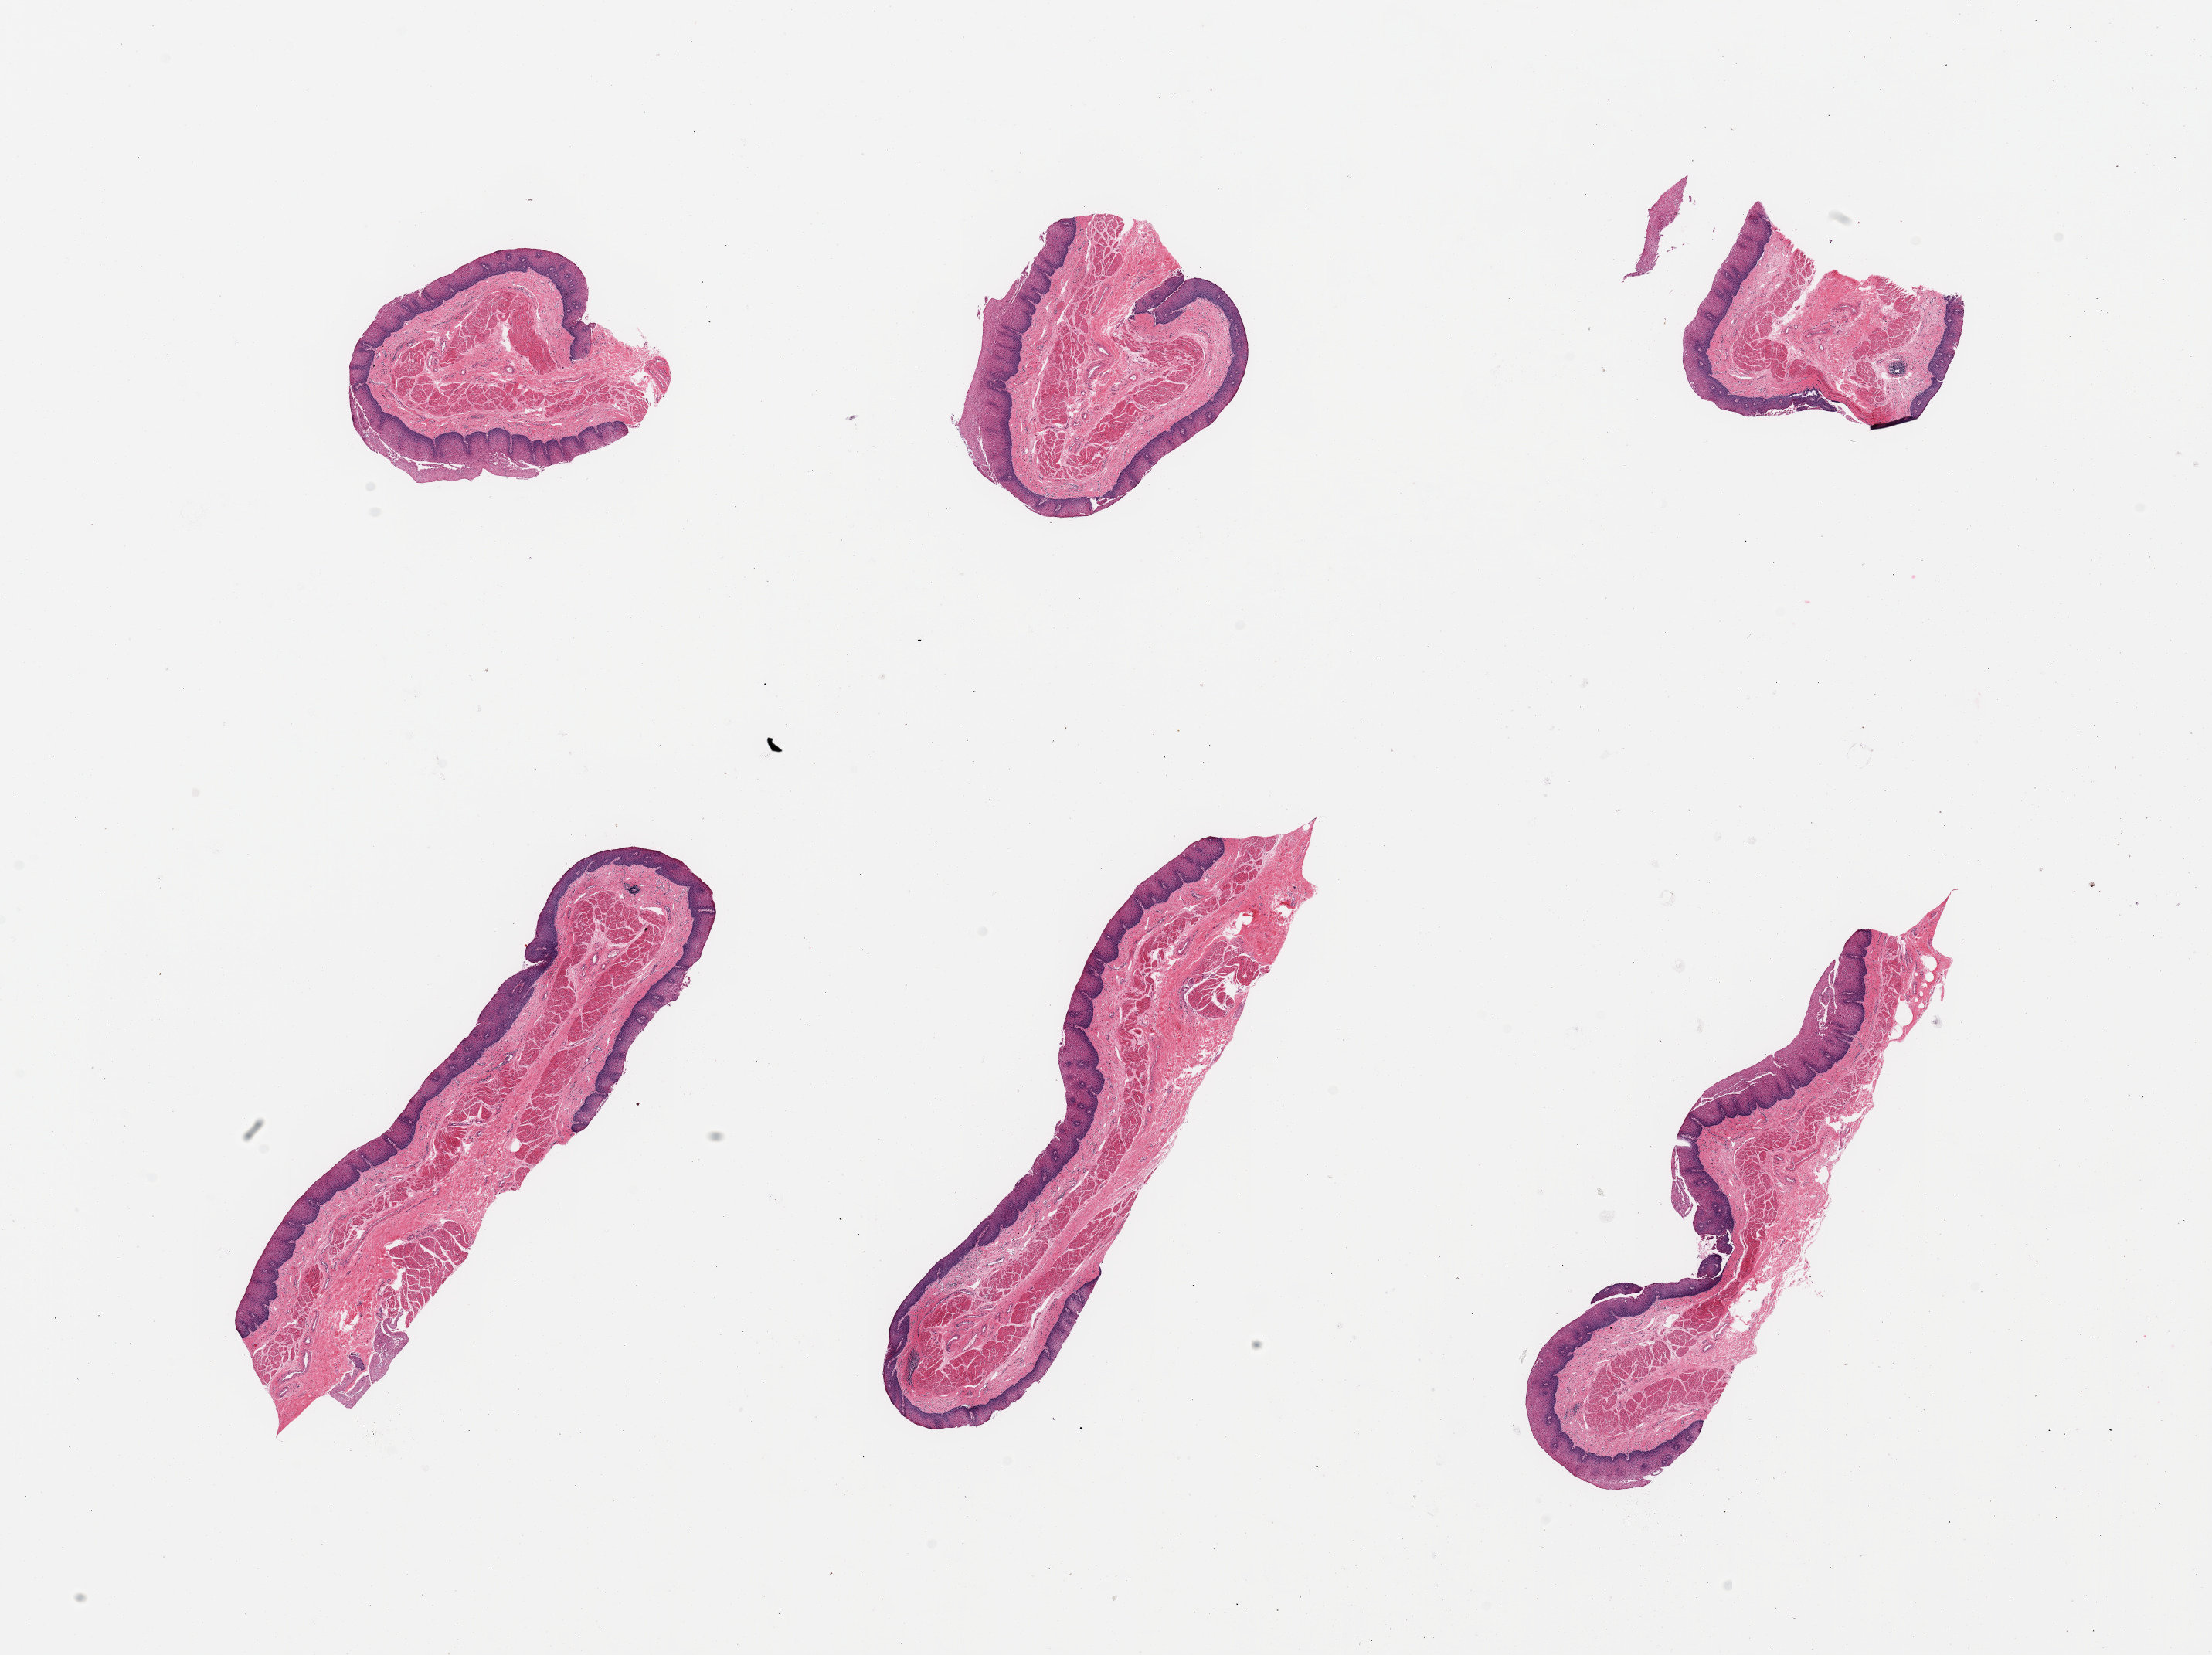
Whole-slide image, hematoxylin and eosin (H&E) stain, whole scanned area (about 22.6 x 16.9 mm) shown as a low-resolution overview. PAXgene-fixed paraffin-embedded (PFPE) section. Section of esophageal mucous membrane (target tissue). Donor tissue sample. Donor sex: male.
* pathologist's review note for this sample: 6 pieces; prominent muscularis mucosae; no submucosal glands